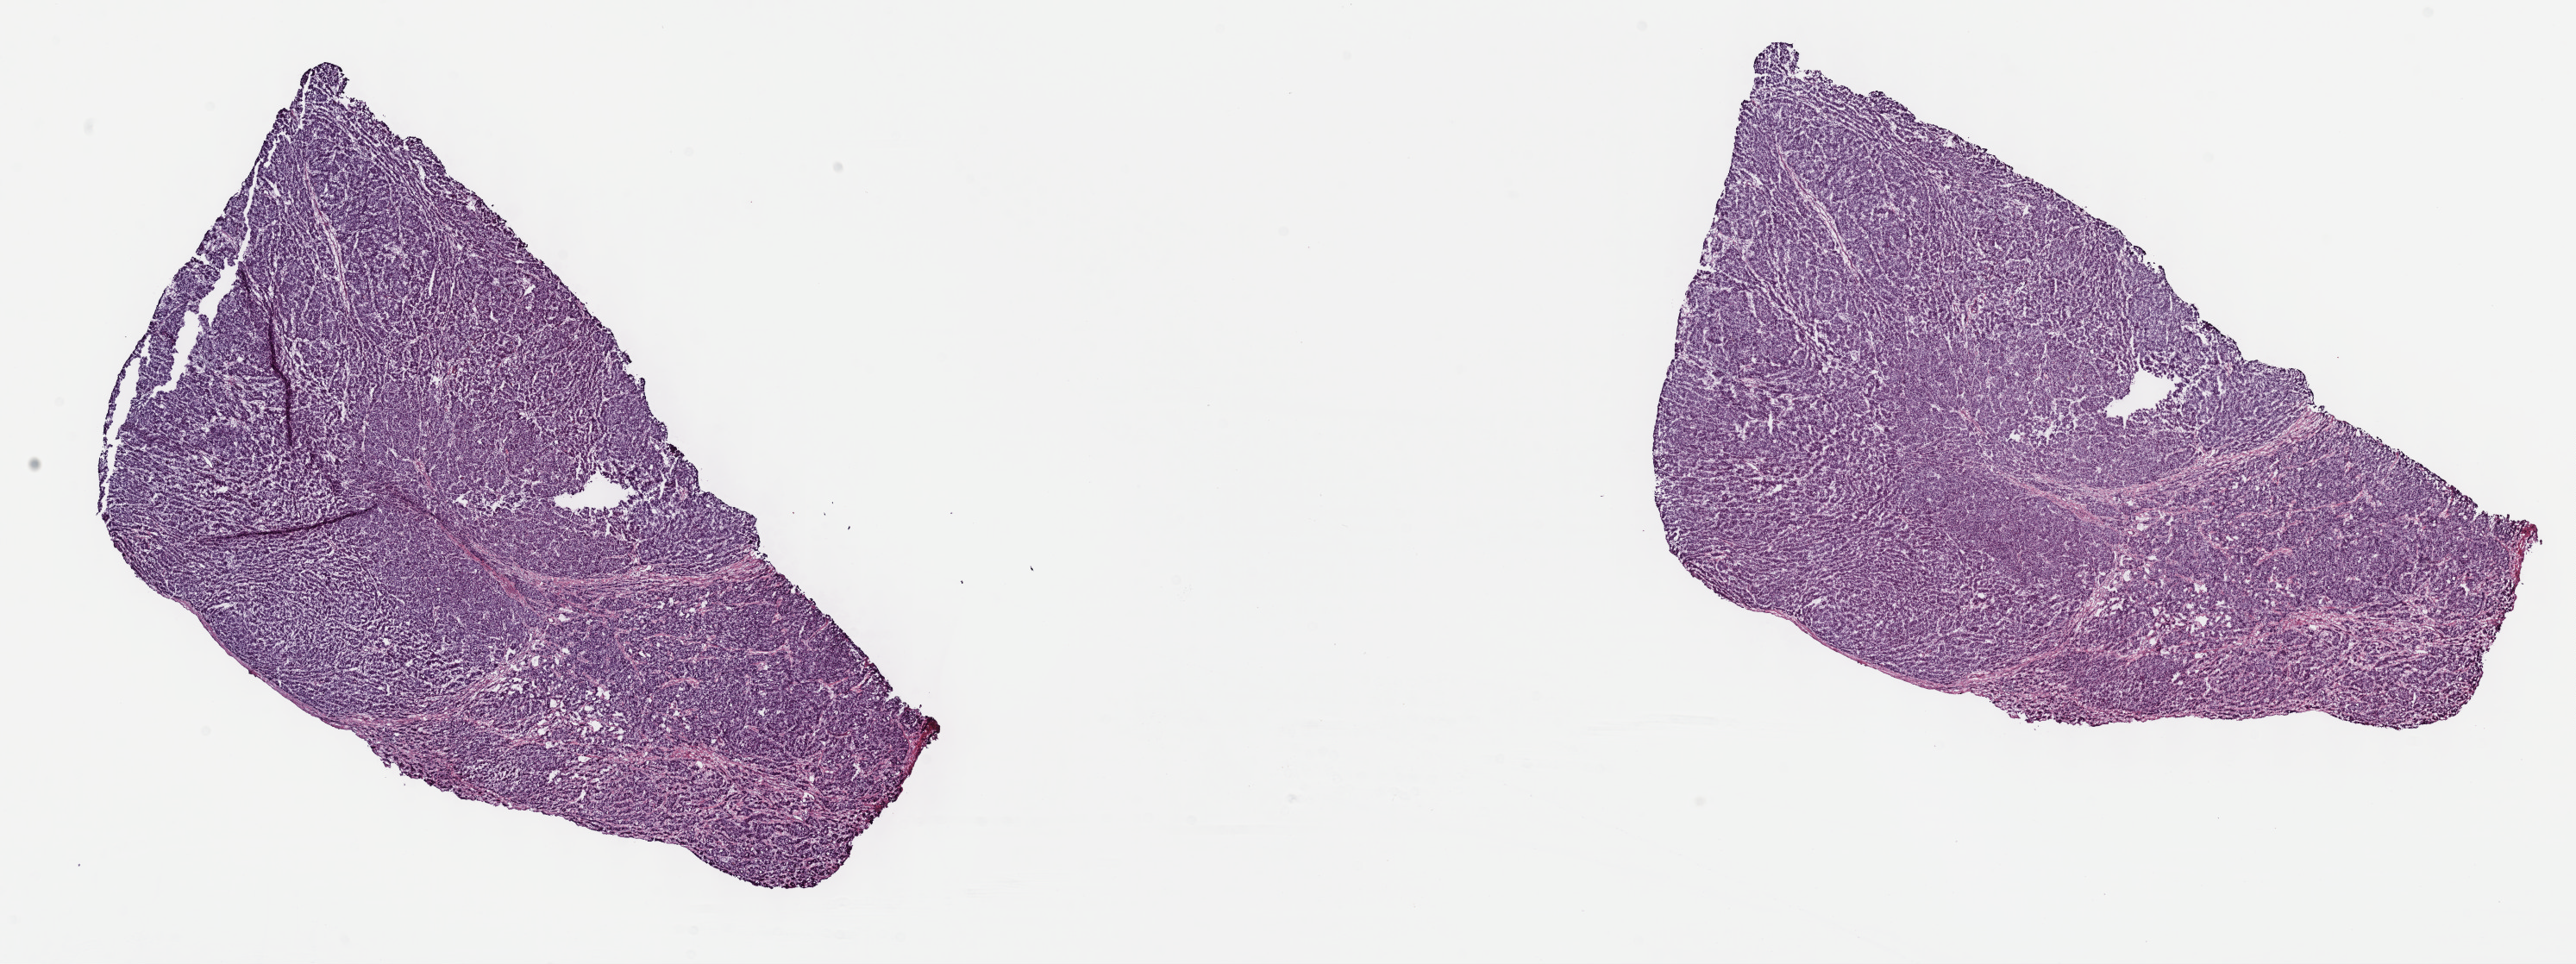
H&E-stained whole-slide image, whole scanned area (about 24.2 x 9.0 mm) shown as a low-resolution overview. Frozen section. Liver, primary tumour sample. Patient: male, age at initial diagnosis 38 years. Histologic grade: G2 (moderately differentiated). Composition of this section per pathologist review: tumour cells 85%, tumour nuclei 85%, normal cells 0%, stromal cells 15%, necrosis 0%. Inflammatory infiltration, as recorded: lymphocyte infiltration 2%, monocyte infiltration 1%, neutrophil infiltration 4%.
* histologic diagnosis: Hepatocellular carcinoma, NOS
* AJCC pathologic stage: I (6th edition)